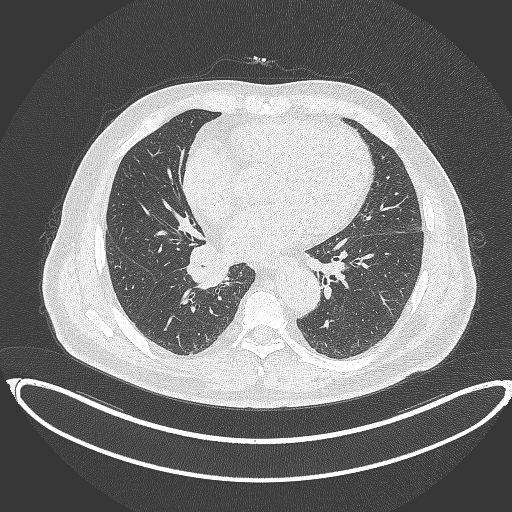
Chest CT, one axial slice; lung window (W 1500 / L -600 HU); 1 mm slice thickness; 512 × 512 image matrix, field of view 448 × 448 mm. Male patient, age 61 years. From the clinical record (not read from this slice): clinical TNM (as recorded): T1b N1 M0.
Structures marked on this image (rectangle marked by the reading radiologist):
- lung tumour (recorded histology: squamous cell carcinoma): bounding box <183,241,230,291> (left, top, right, bottom; pixels)